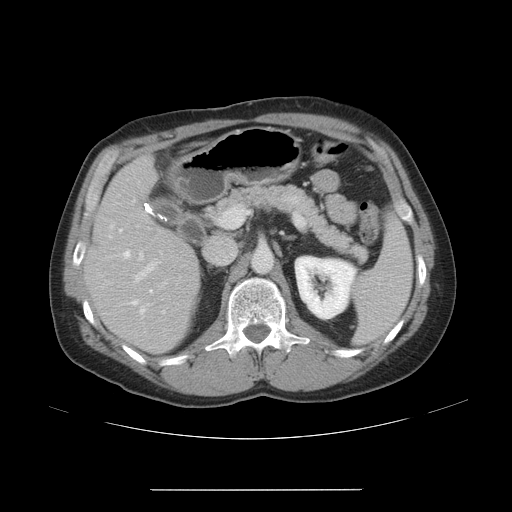
Contrast-enhanced abdominal CT, one axial slice. Position 26 of 48 along the scan axis. Reconstruction kernel STANDARD. Intravenous contrast given. Soft-tissue window (W 400 / L 40 HU). 5 mm slice thickness. 512 × 512 image matrix, field of view 409 × 409 mm. Male patient, age 56 years. Case-level facts recorded for this patient, not image findings: diagnosis: colorectal cancer liver metastases, imaged before liver resection; multiple liver metastases: yes; largest metastasis: 1.8 cm; disease in both lobes: yes.
Annotated regions visible in this slice (outlined manually by an expert reader):
- hepatic veins: bounding box [x1, y1, x2, y2] px = [108, 181, 164, 319]
- liver: [86, 159, 200, 351]
- planned liver remnant (the part of the liver to remain after resection): [89, 159, 200, 351]
- portal vein (with intrahepatic branches): [118, 213, 221, 283]